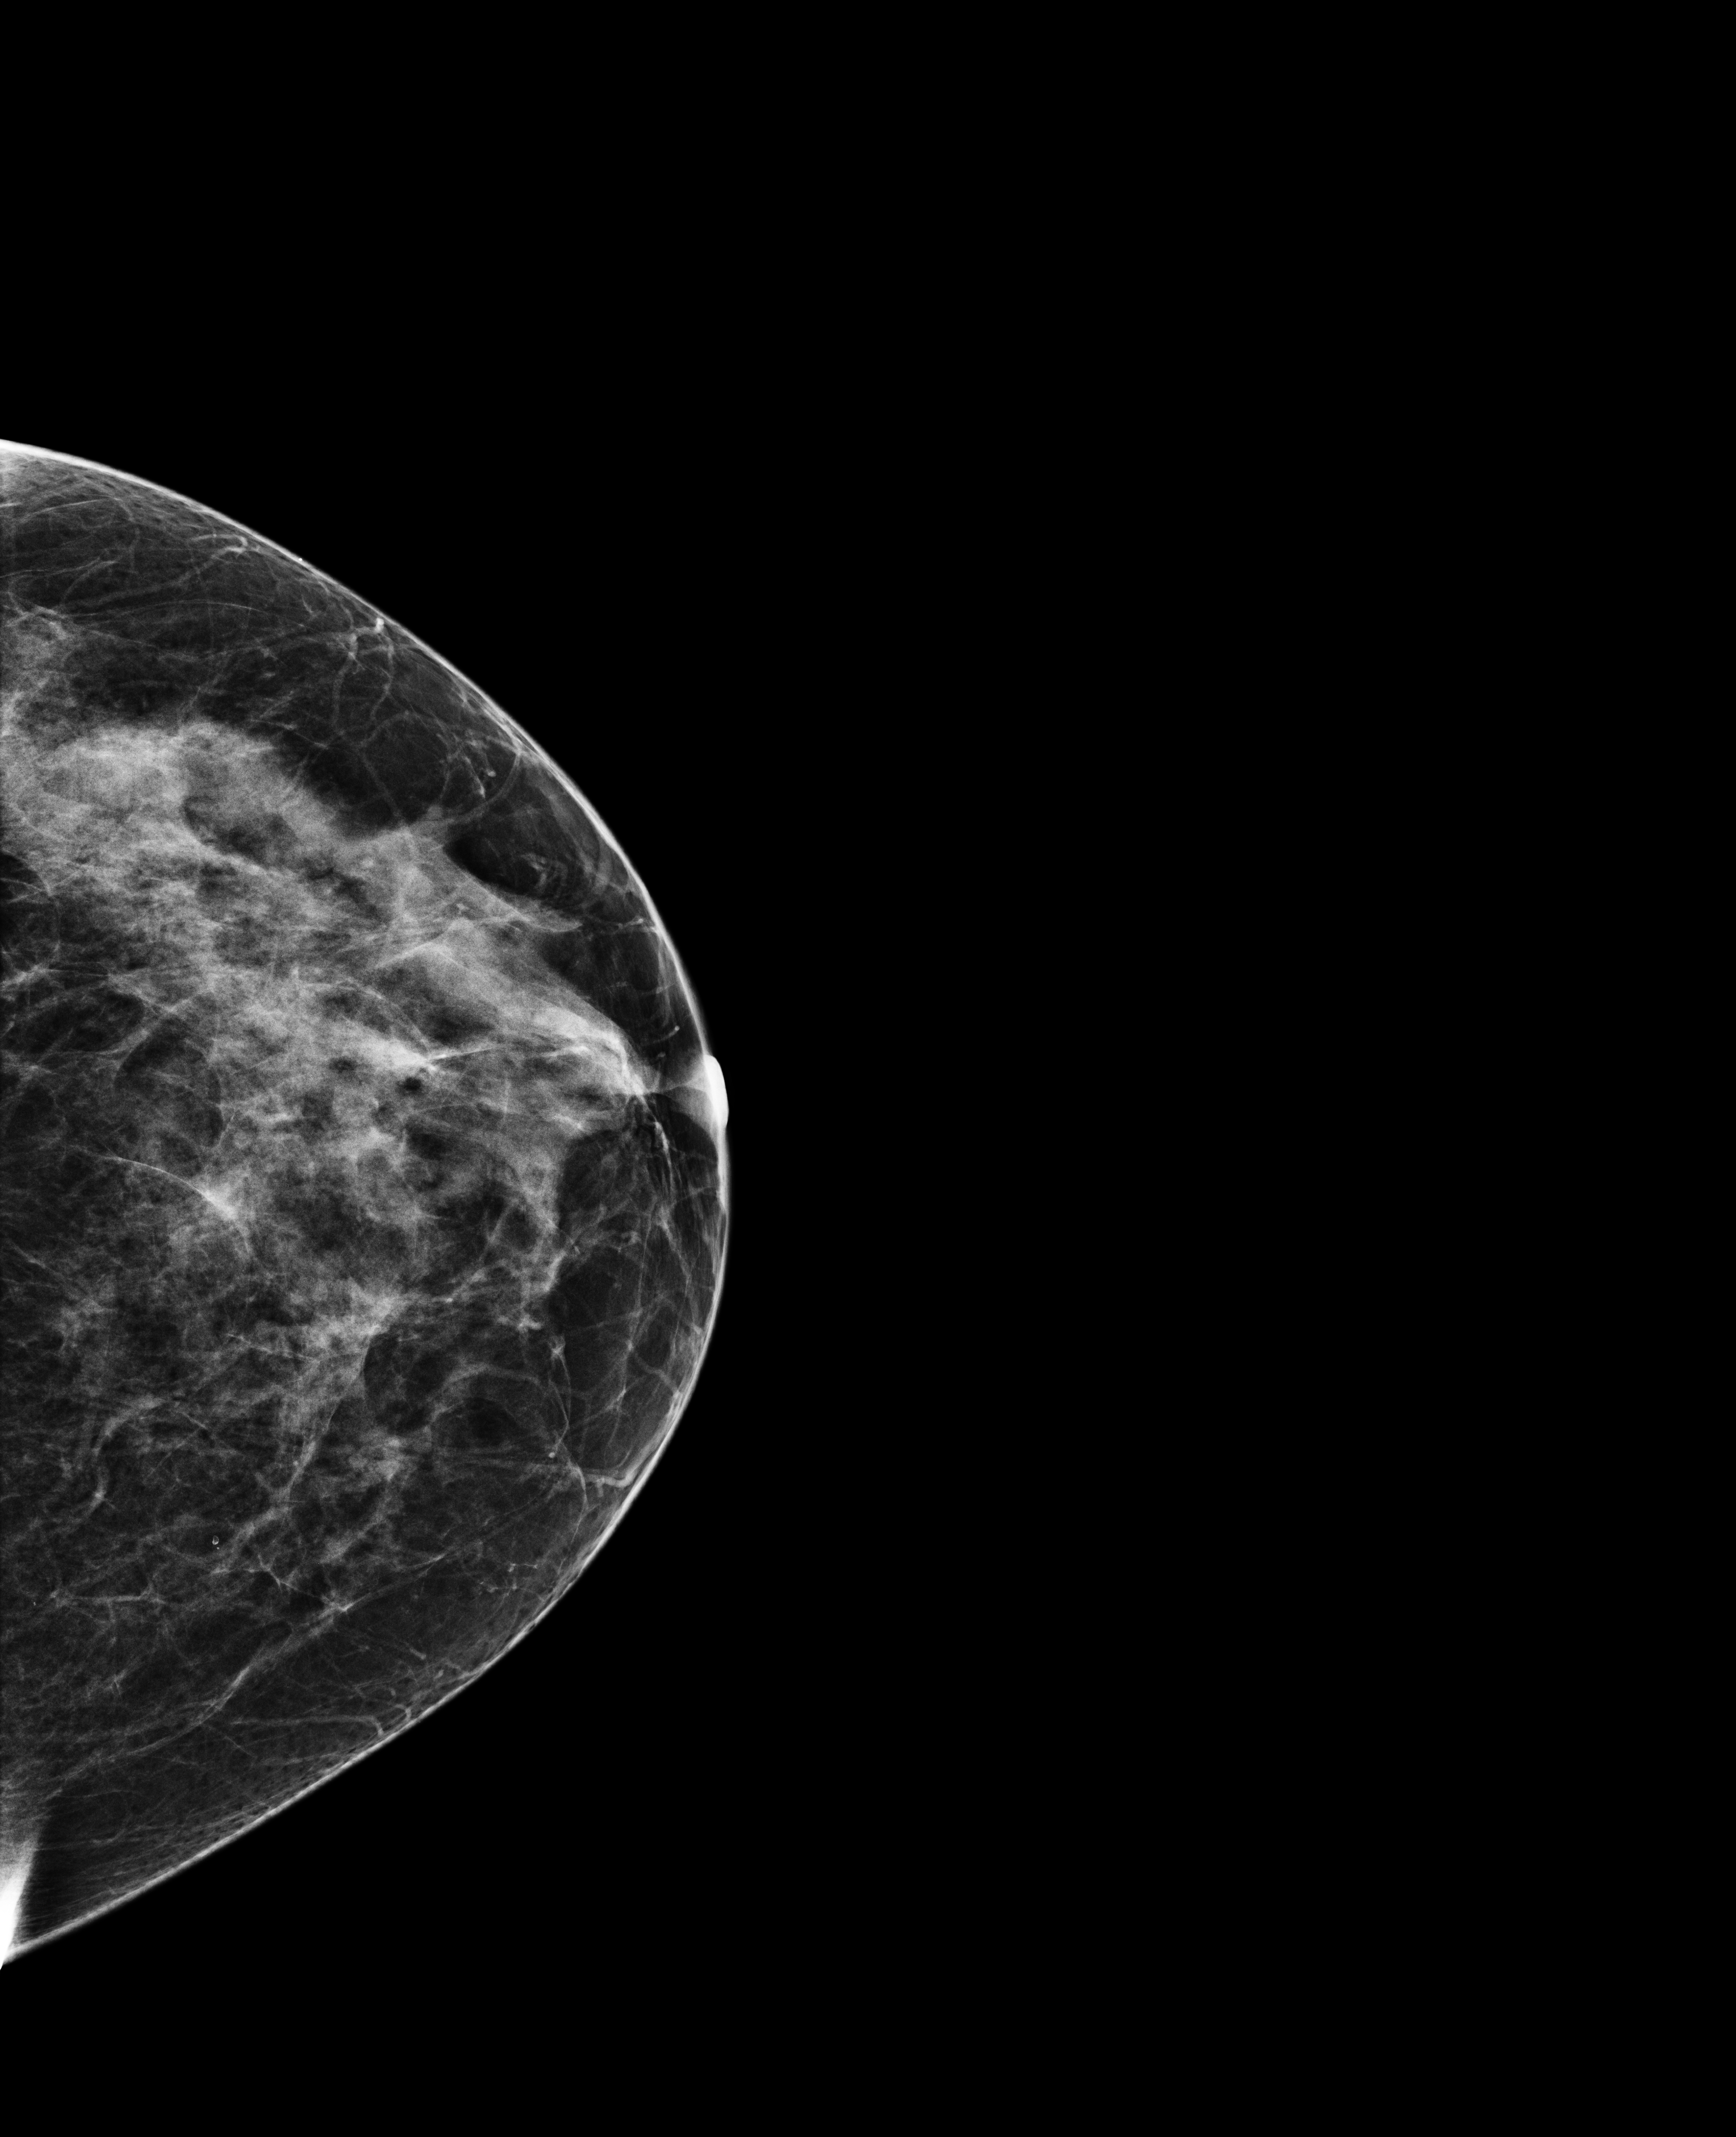
Digital mammogram (FFDM), left breast, cranio-caudal projection, annual screening mammography examination, compressed breast thickness 48 mm. Female patient, age 48 years.
Breast density at the screening exam (both breasts): heterogeneously dense (BI-RADS density category c). Final BI-RADS category for the screening round (tomosynthesis exam, both breasts): category 1. Recall: no recall after this screen.